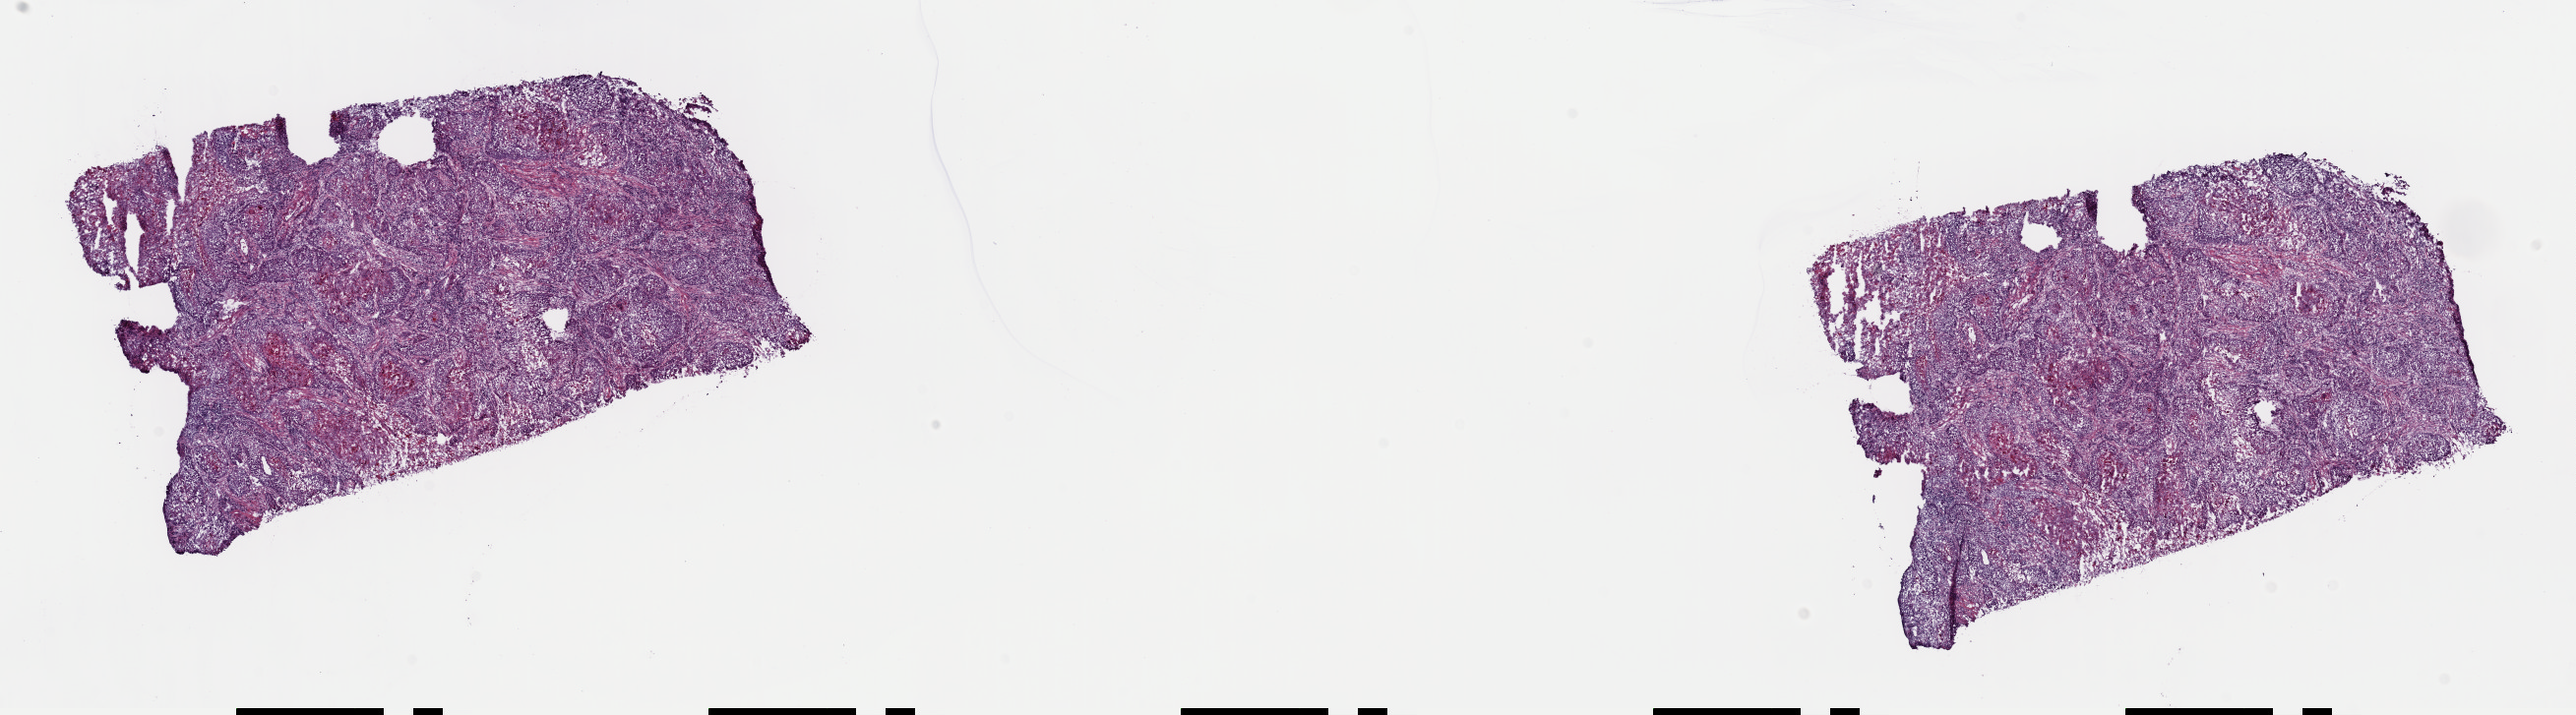
Whole-slide histology image, H&E, shown as a low-resolution overview of the whole scanned area (about 20.7 x 5.7 mm); frozen section from the top of the tissue portion; primary tumour sample from the lung. Patient: female, age at initial diagnosis 70 years.
Pathologic diagnosis: Squamous cell carcinoma, NOS (upper lobe, lung).